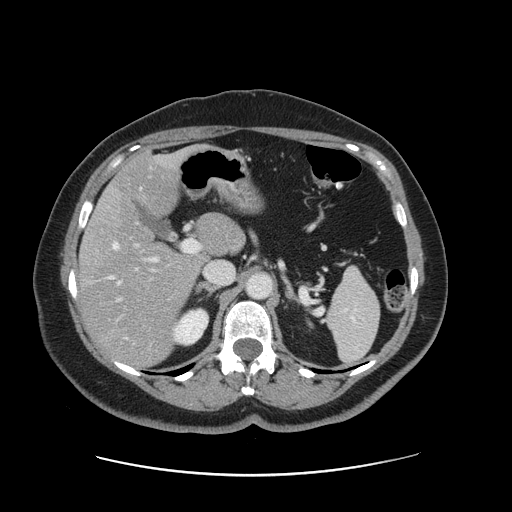
Contrast-enhanced abdominal CT, one axial slice. Slice 85 of 161 in the series (ordered by position). 120 kVp. Soft-tissue window (W 400 / L 40 HU). 2.5 mm slice thickness. 512 × 512 image matrix, field of view 398 × 398 mm. Female patient, age 62 years. From the clinical record (not read from this slice): diagnosis: colorectal cancer liver metastases, imaged before liver resection; multiple liver metastases: no; largest metastasis: 2.5 cm; chemotherapy before resection: yes.
Structures marked on this image (outlined manually by an expert reader):
- hepatic veins: bounding box <110,187,142,285> (left, top, right, bottom; pixels)
- liver: <80,152,241,366>
- planned liver remnant (the part of the liver to remain after resection): <110,153,241,260>
- portal vein (with intrahepatic branches): <115,239,200,321>